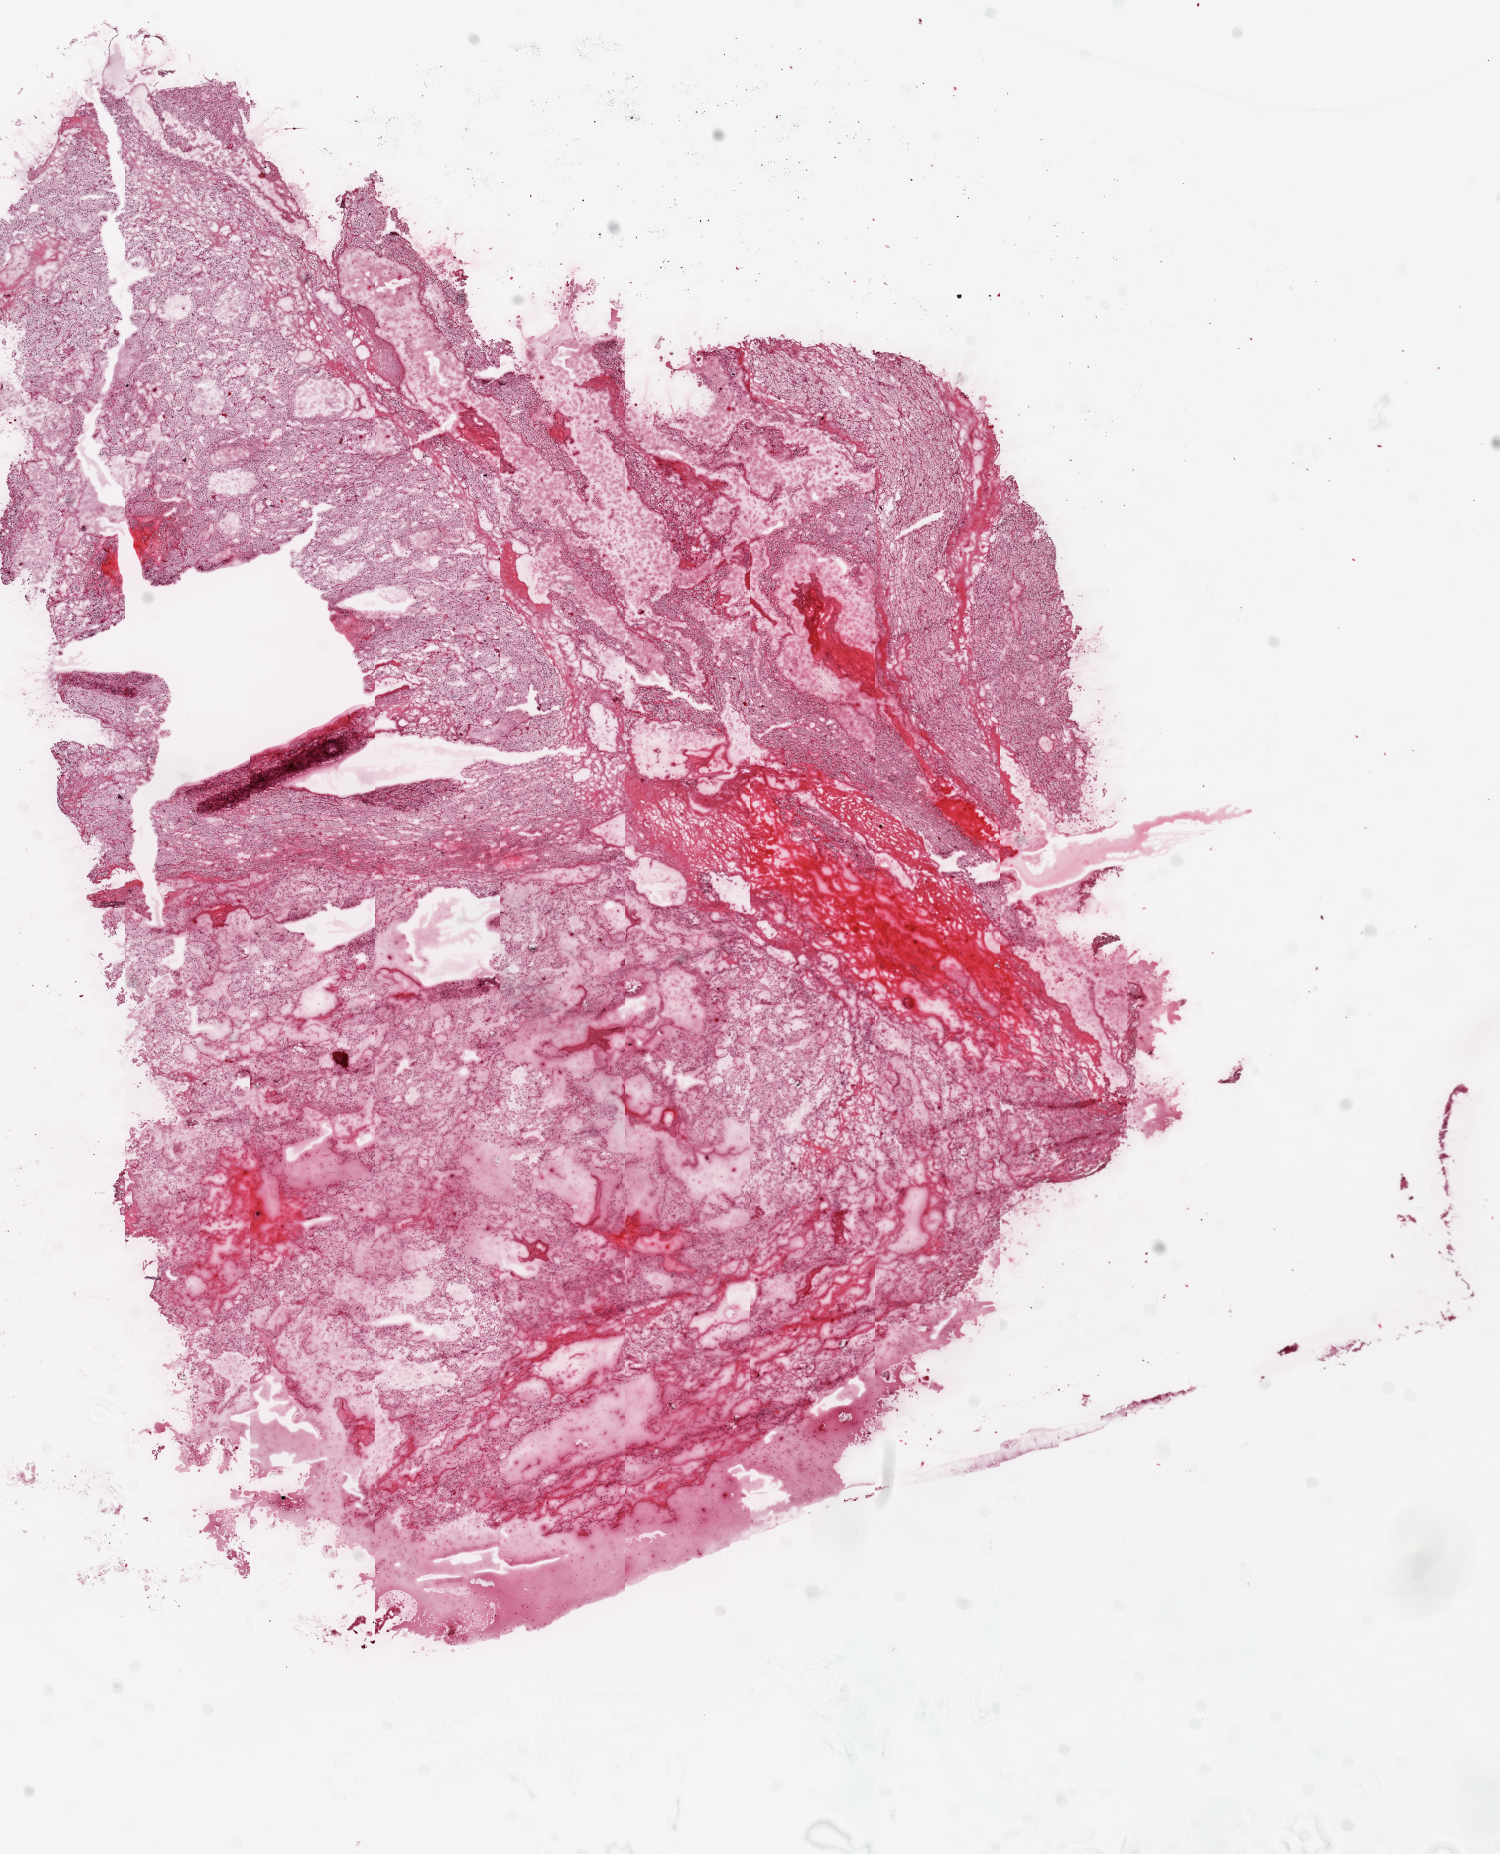
Whole-slide histology image, Hematoxylin and eosin (H&E) stained, shown as a low-resolution overview of the whole scanned area (about 12.0 x 14.9 mm, acquisition: 20x scan), frozen section from the top of the tissue portion, primary tumour sample from the kidney. Patient: female, age at initial diagnosis 54 years. Histologic grade: G2 (moderately differentiated). Pathologist review of this section (percent, as recorded): tumour cells 85%, tumour nuclei 85%, normal cells 0%, stromal cells 15%, necrosis 0%.
Lymph nodes positive (case pathology): 0 of 11 examined. Pathologic diagnosis: Clear cell adenocarcinoma, NOS. AJCC pathologic stage: I.